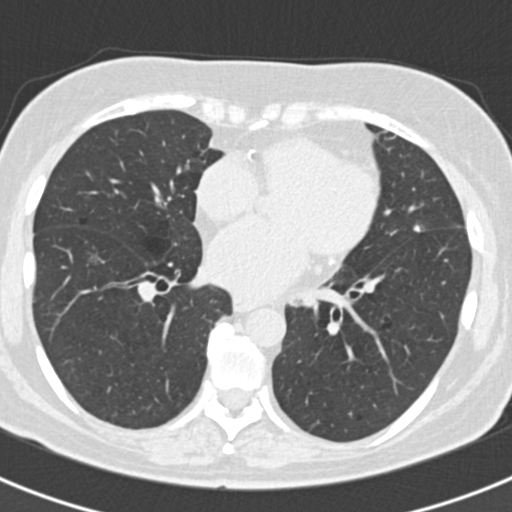
Low-dose screening chest CT, axial slice, baseline screening round, lung window (W 1500 / L -600 HU), 2 mm slice thickness, 120 kVp, slice 115 of 184 in the series, 512 × 512 image matrix. Female, age 60 years at enrolment.
Lesion marked by an expert reader, box from (x=399, y=215) to (x=440, y=248) px. The screening reader recorded 3 non-calcified nodules or masses ≥4 mm on this exam (lingula, left lower lobe, lingula); which of them this box marks is not recorded. Later outcome: lung cancer diagnosed 886 days after this screen — non-small cell carcinoma, left upper lobe, poorly differentiated (G3), stage IB (AJCC 6th edition), 7 mm at pathology.